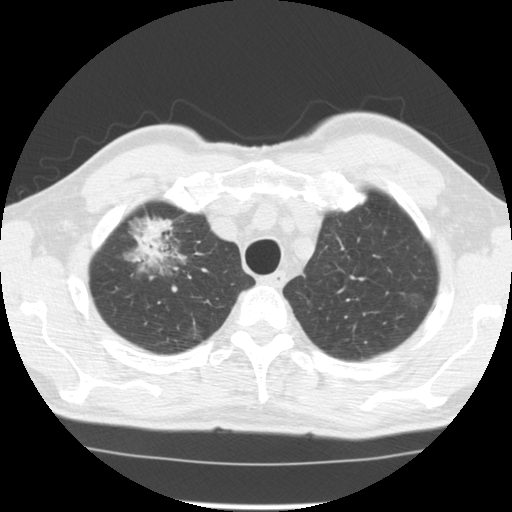
Low-dose screening chest CT, one axial slice. Position 105 of 128 along the scan axis. 120 kVp. Lung window (W 1500 / L -600 HU). 512 × 512 image matrix, field of view 340 × 340 mm.
Structures marked on this image (expert manual segmentation):
- lesion 1 (tumor, upper lobe of right lung): box from (x=137, y=219) to (x=172, y=257) px